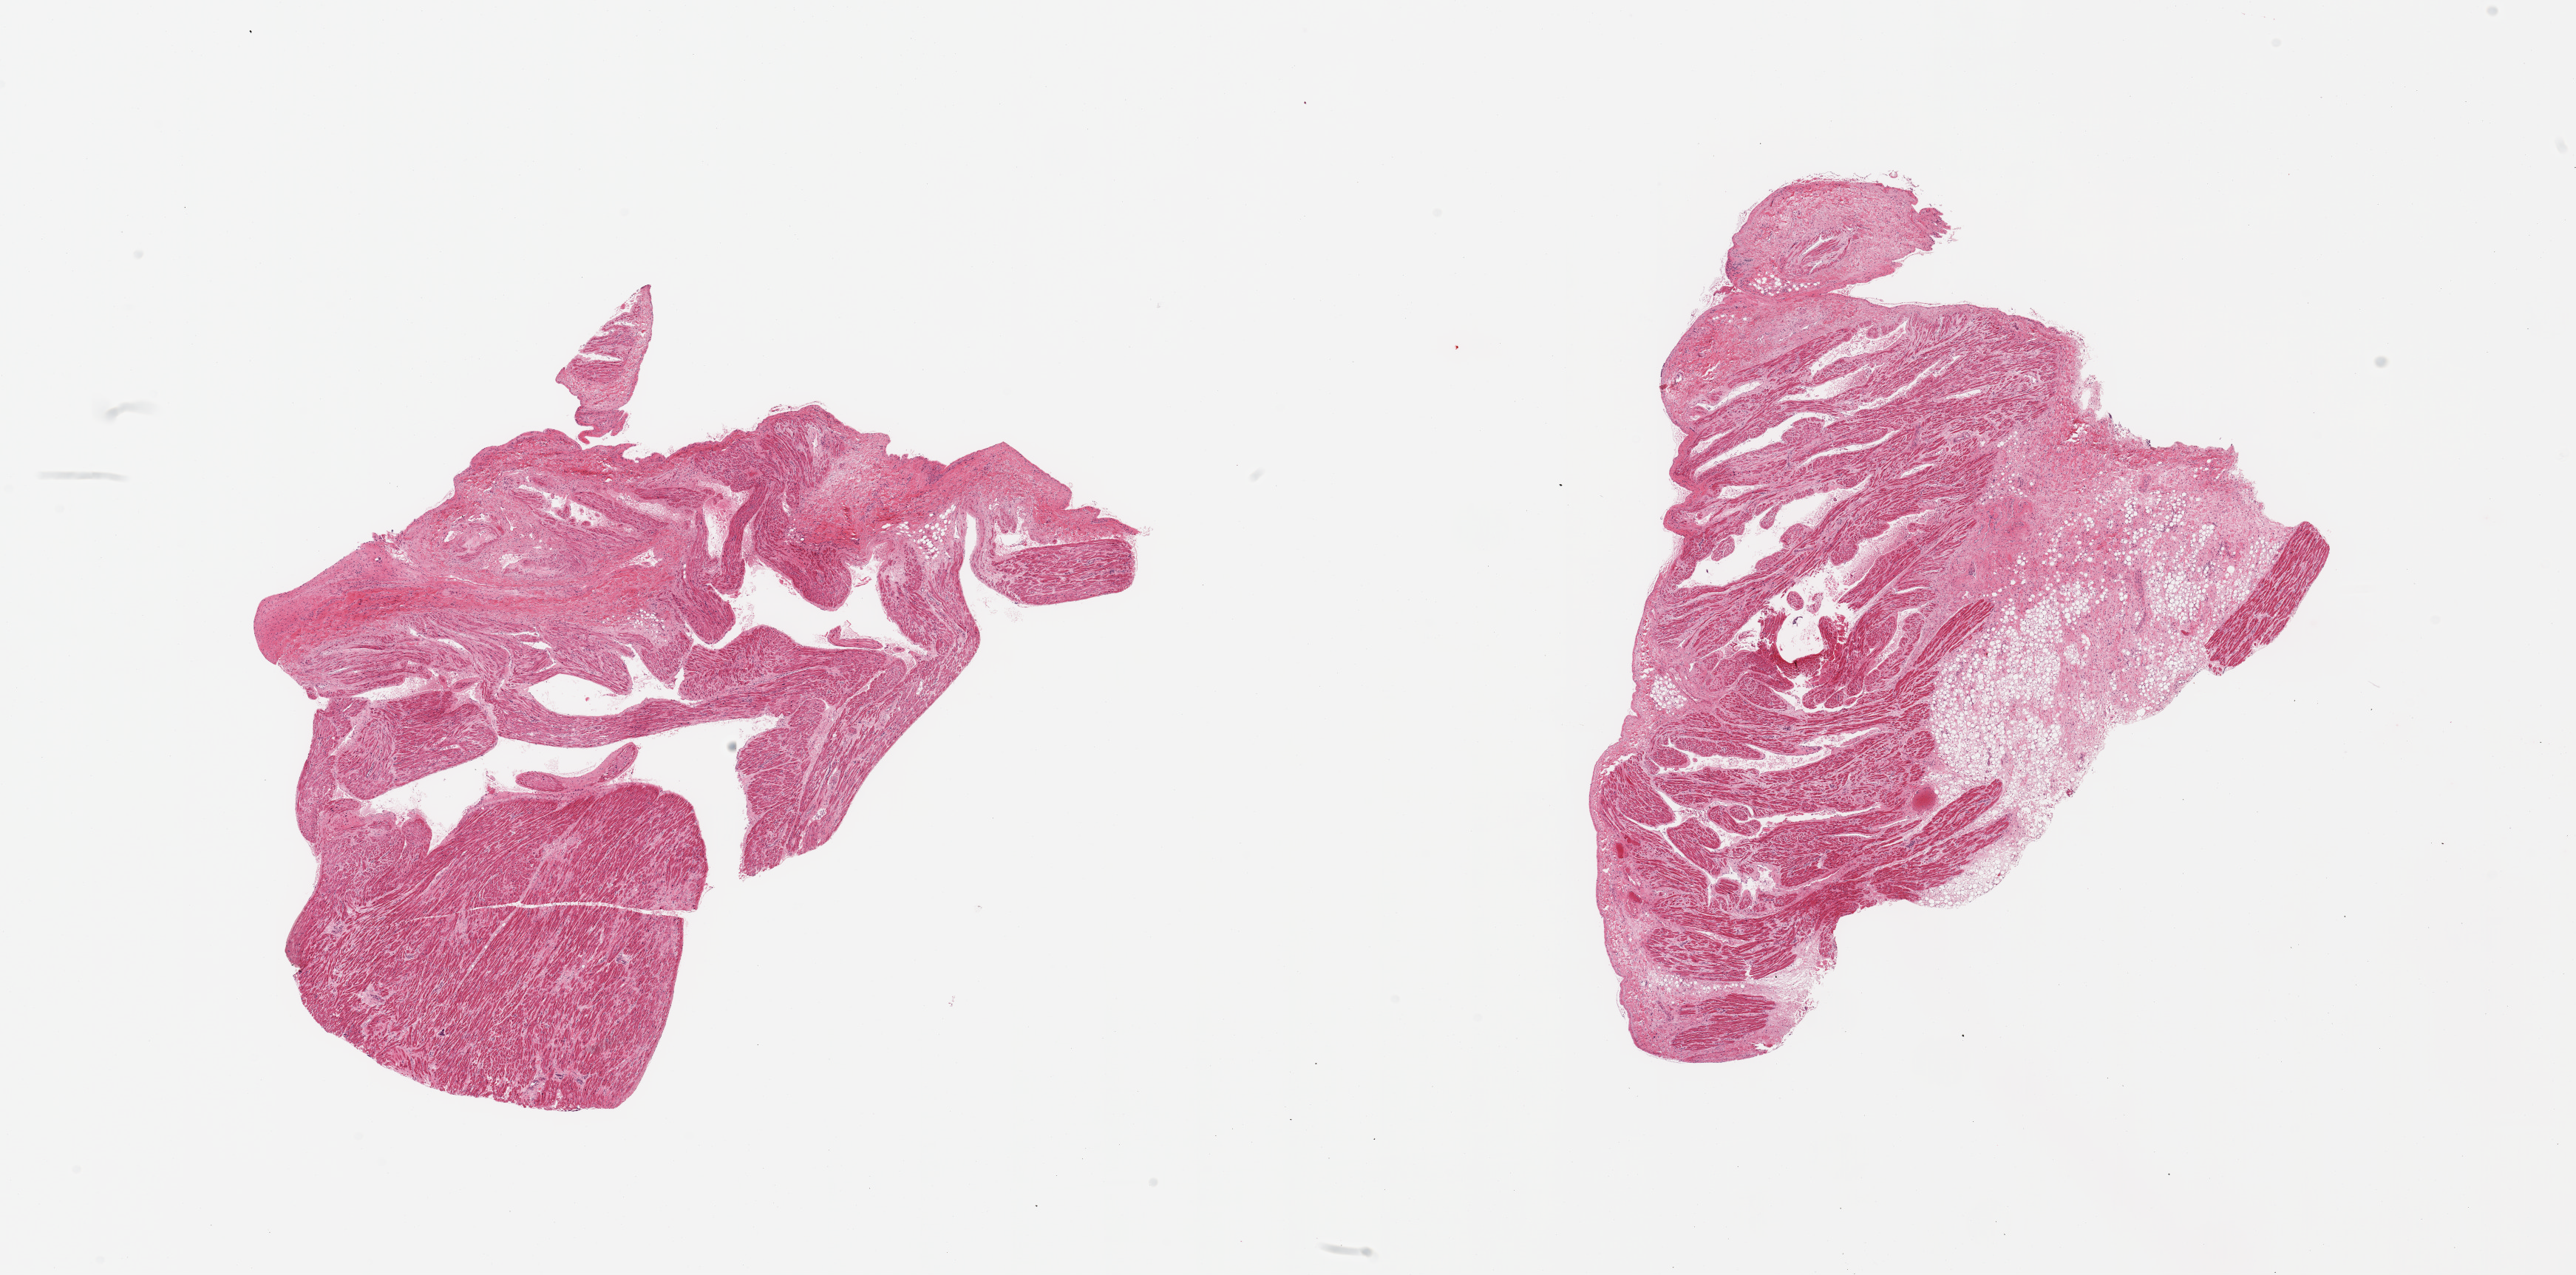
Digitized haematoxylin and eosin-stained section, brightfield, low-resolution overview of the scanned area, about 27.6 x 13.6 mm (acquisition: 20x scan), PAXgene-fixed, paraffin-embedded tissue, target tissue: auricular appendage, donor tissue sample.
Review note (as recorded): 2 pieces, no abnormalities.